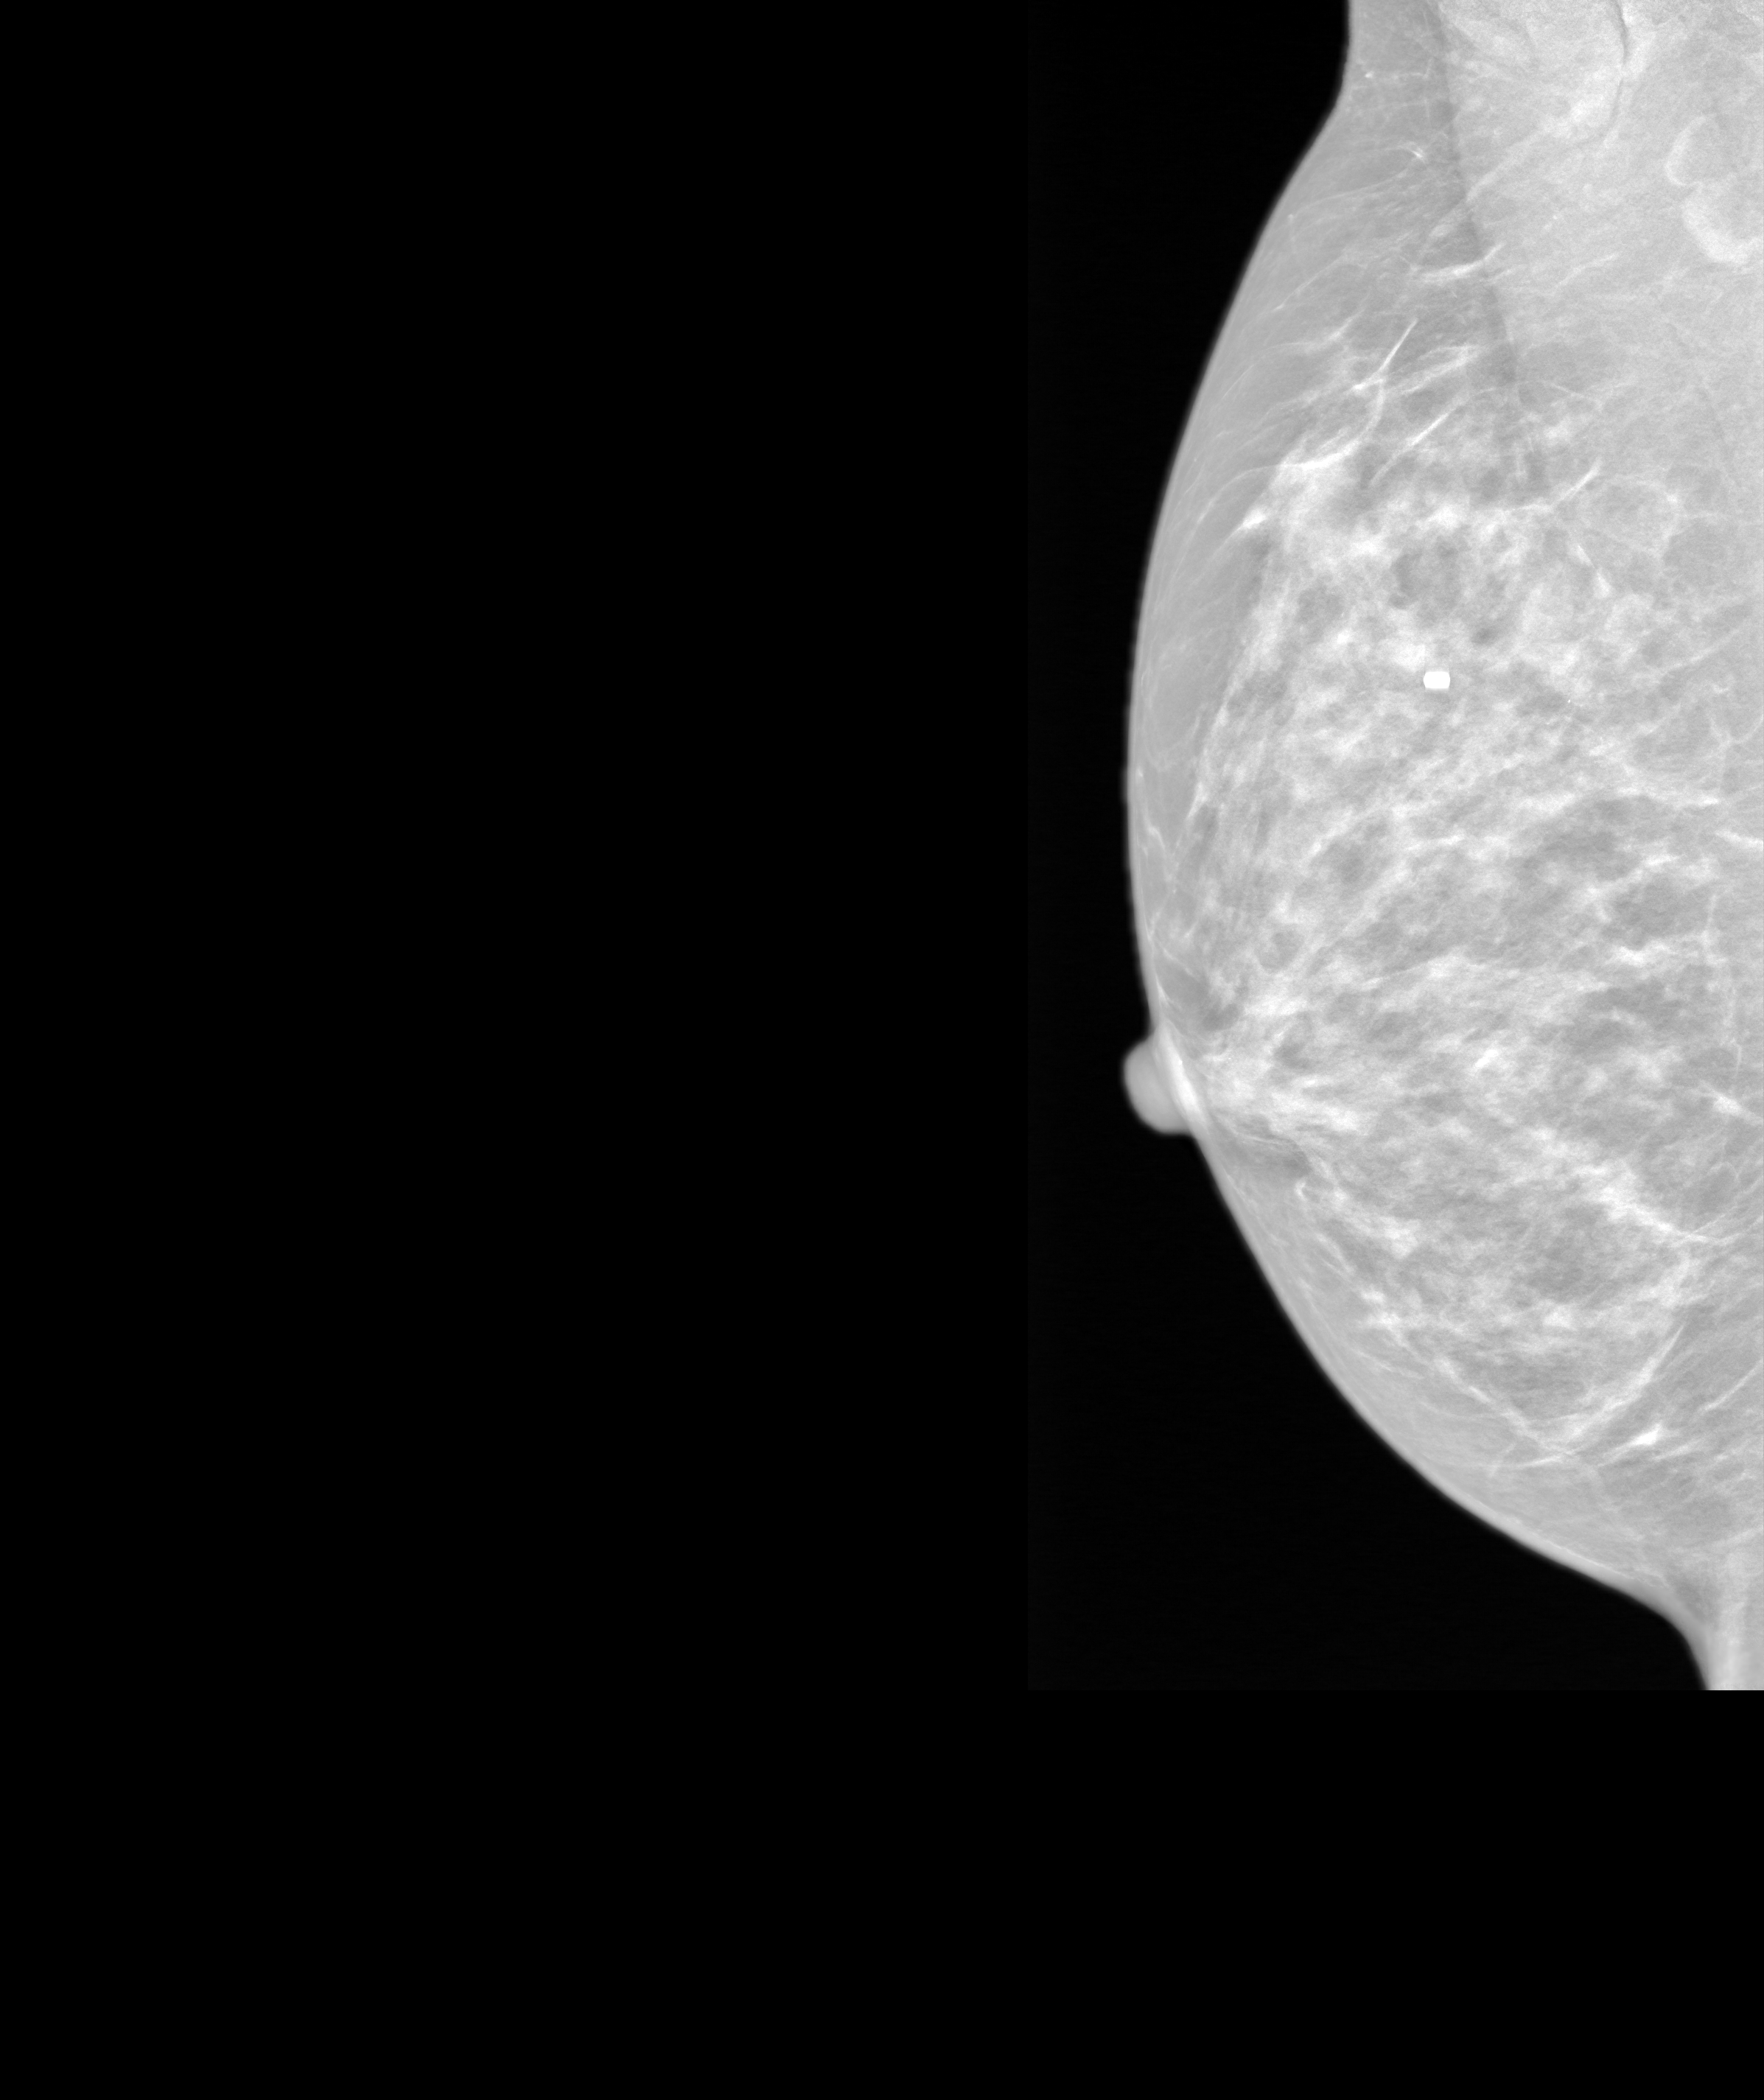
Annual screening mammography examination. Patient aged 57 years (female).
Image type: synthesized 2-D view from tomosynthesis. Breast: right. Projection: MLO view.